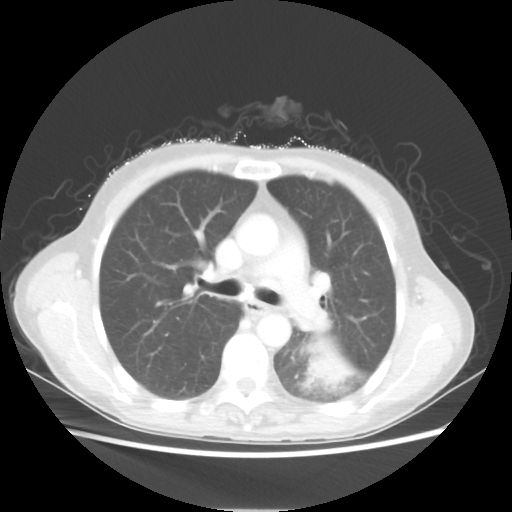
Chest CT, one axial slice; position 35 of 56 along the scan axis; reconstruction kernel STANDARD; 80 kVp; lung window (W 1500 / L -600 HU); 512 × 512 image matrix. Patient: female, 53 years. From the clinical record (not read from this slice): clinical TNM (as recorded): T3 N0 M0.
Annotated regions visible in this slice (rectangle marked by the reading radiologist):
- lung tumour (recorded histology: adenocarcinoma): bounding box (x1, y1, x2, y2) in pixels: (304, 341, 353, 389)